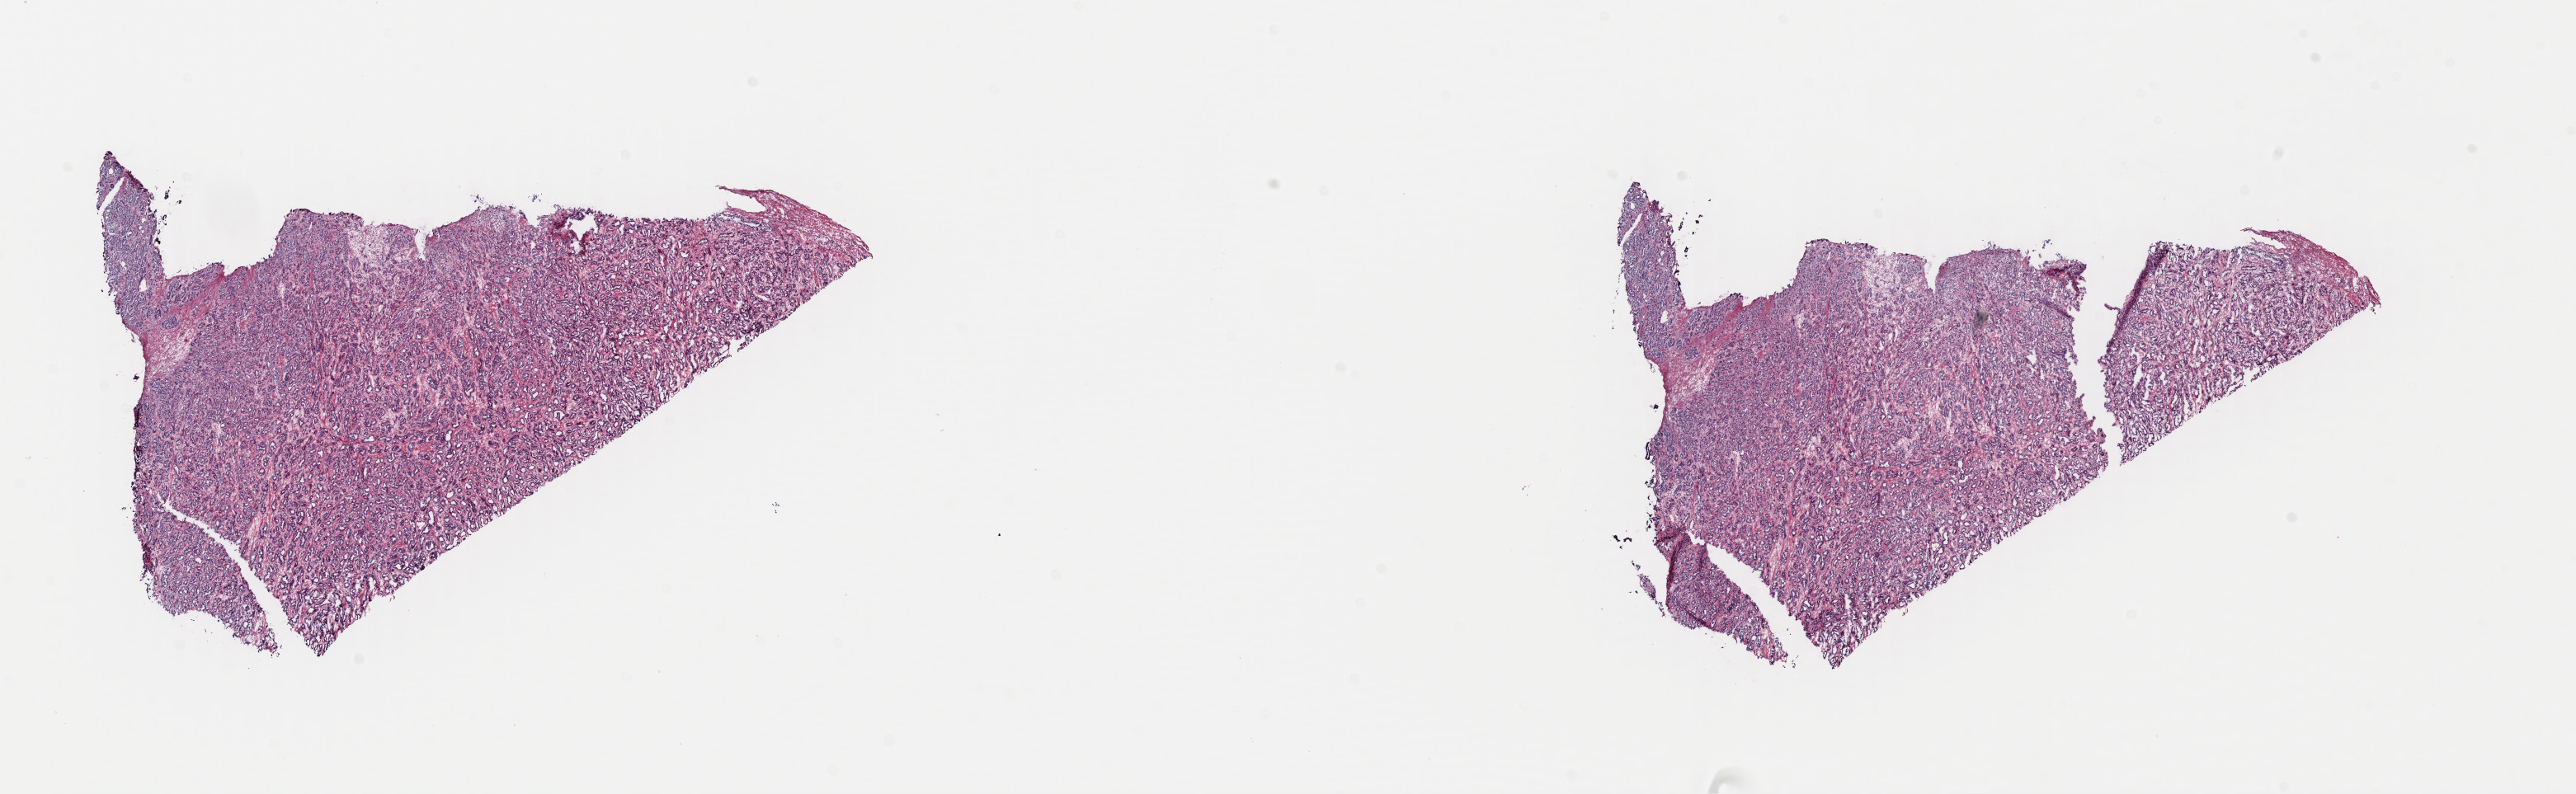
Whole-slide histology image, H&E-stained, a low-resolution overview of the entire scanned area, about 24.6 x 7.6 mm, frozen section from the top of the tissue portion, prostate, primary tumour sample. Patient: male, age at initial diagnosis 54 years. Gleason score: 7 (3+4). Pathologist review of this section (percent, as recorded): tumour cells 100%, tumour nuclei 90%, normal cells 0%, stromal cells 0%, necrosis 0%. Inflammatory infiltration, as recorded: lymphocyte infiltration 0%, monocyte infiltration 0%, neutrophil infiltration 0%.
* diagnosis: Adenocarcinoma, NOS (prostate gland)